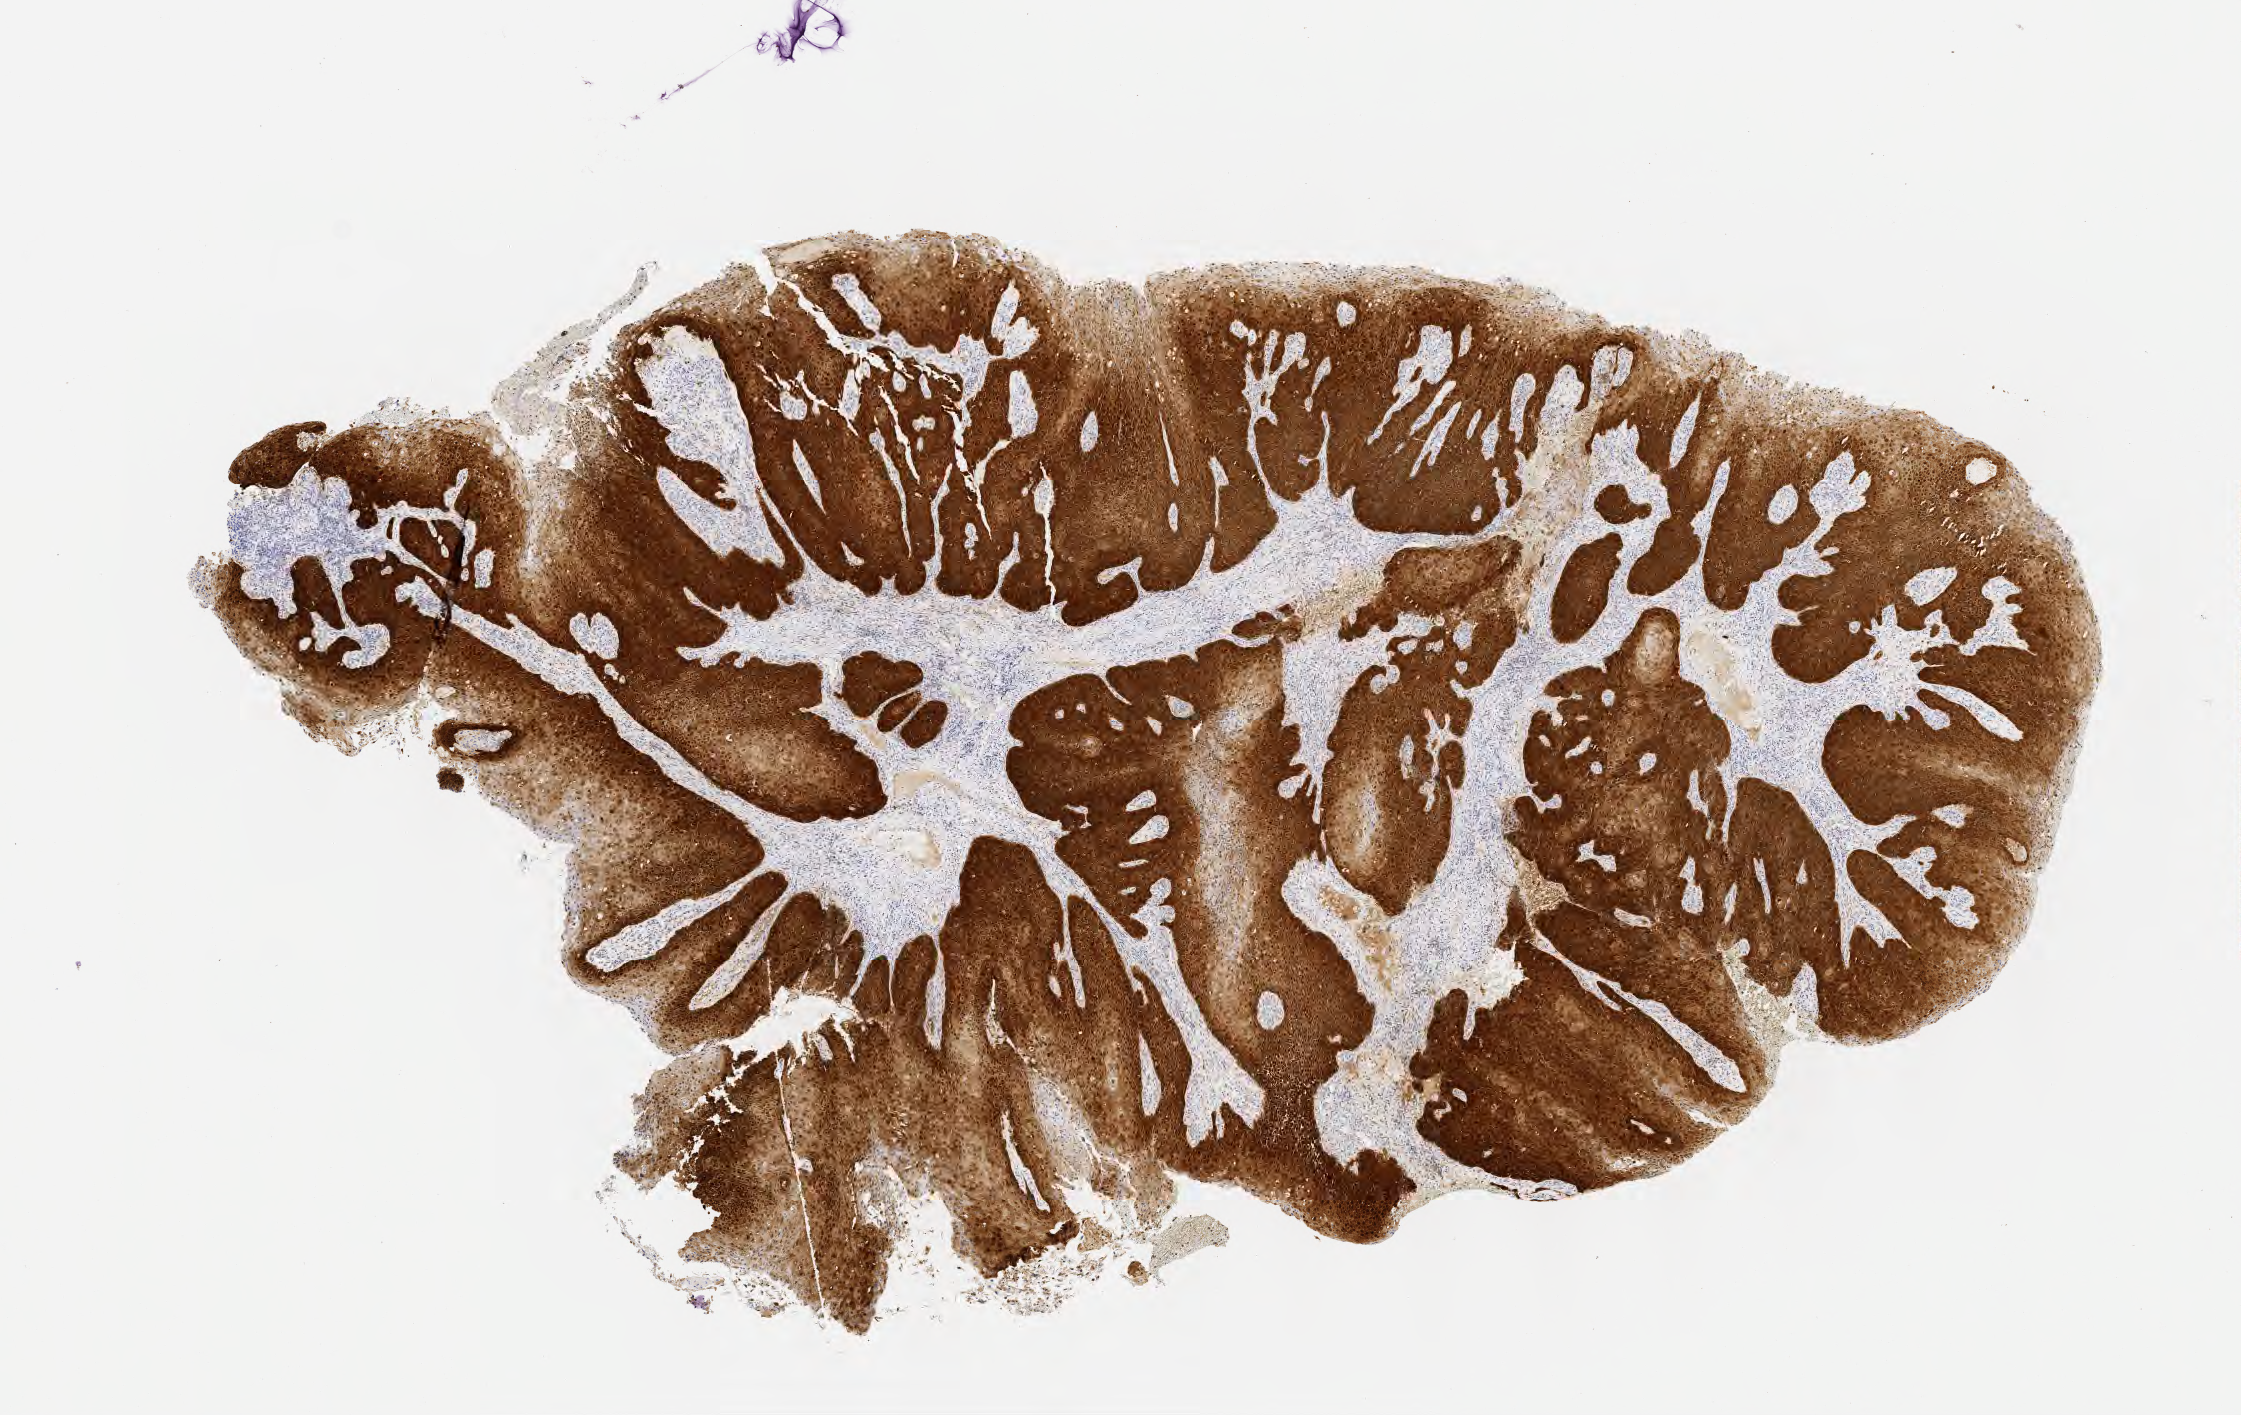
Immunohistochemistry (IHC) whole-slide image stained for p16 (p16INK4a) — whole scanned area (about 9.1 x 5.7 mm) shown as a low-resolution overview; tumor tissue; anatomic site: cervix. Patient female; aged 54.
- histologic diagnosis: Squamous cell carcinoma, large cell, nonkeratinizing, NOS